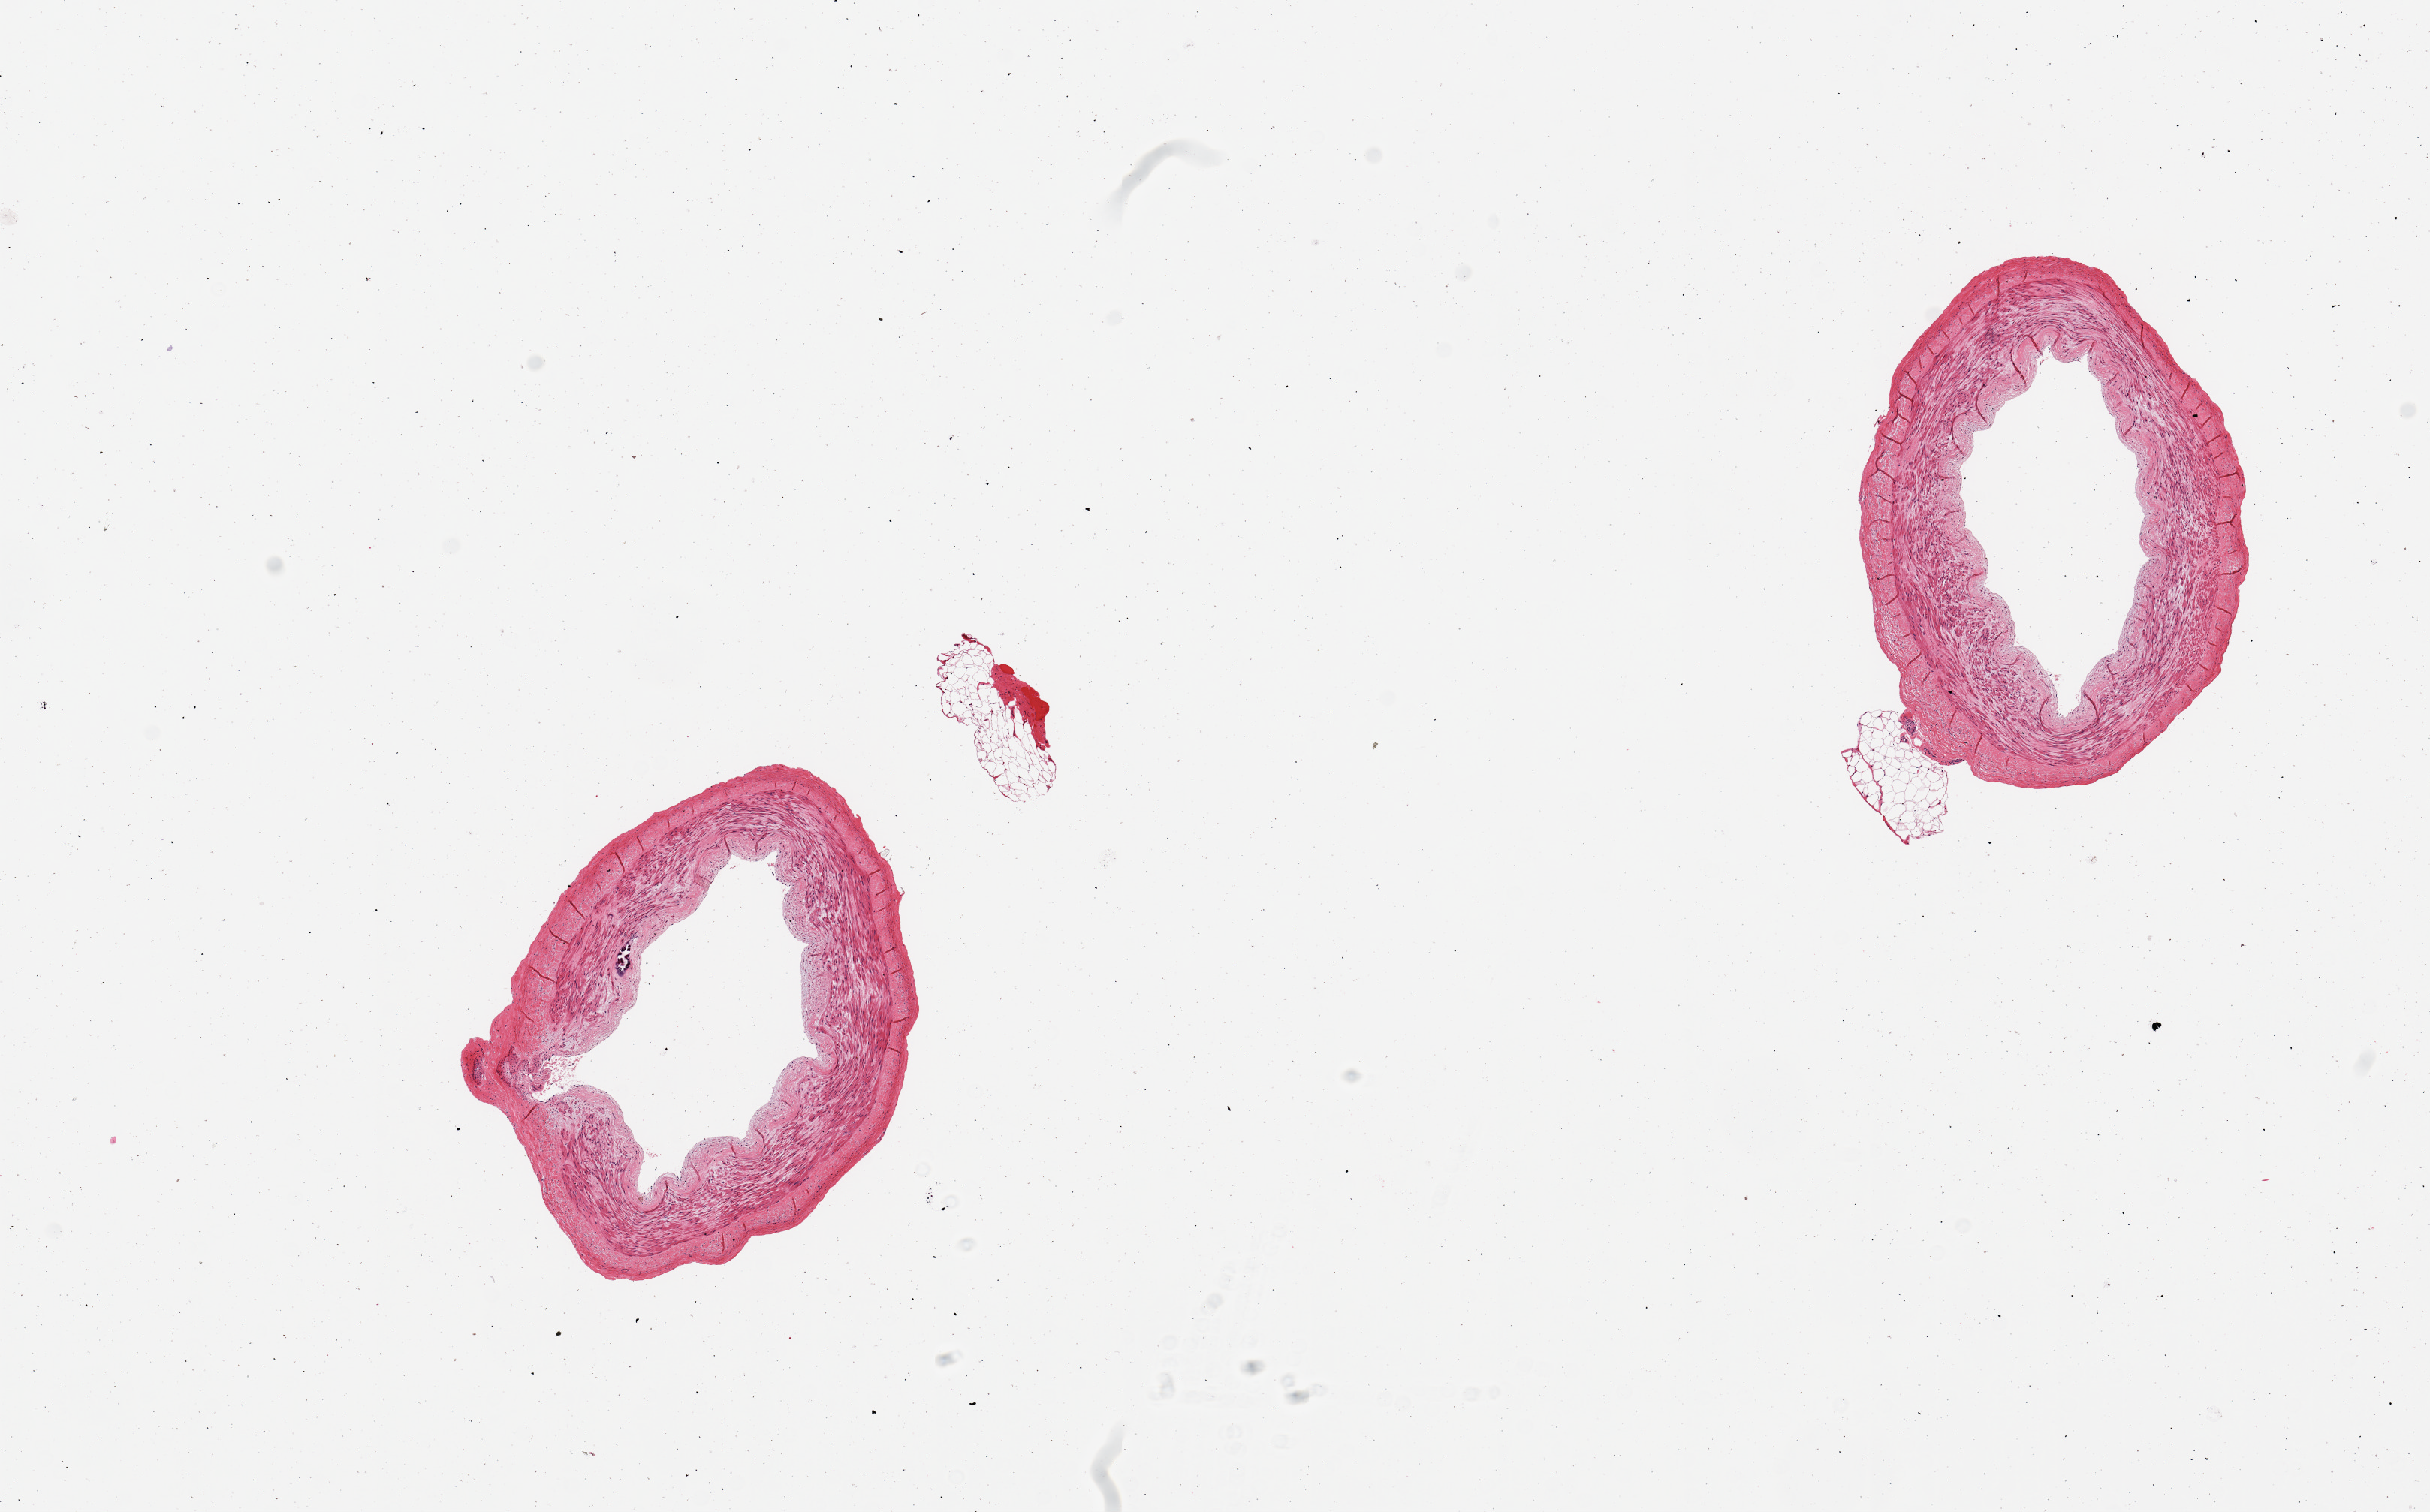
Whole-slide image, haematoxylin and eosin stain, brightfield — shown as a low-resolution overview of the whole scanned area (about 12.8 x 8.0 mm, from a 20x scan), PAXgene-fixed, paraffin-embedded tissue, section of tibial artery (target tissue), tissue donor sample. Donor: female.
Reviewer comment on this tissue sample: 2 pieces, good clean specimens, no adherent fat, no atherosis.